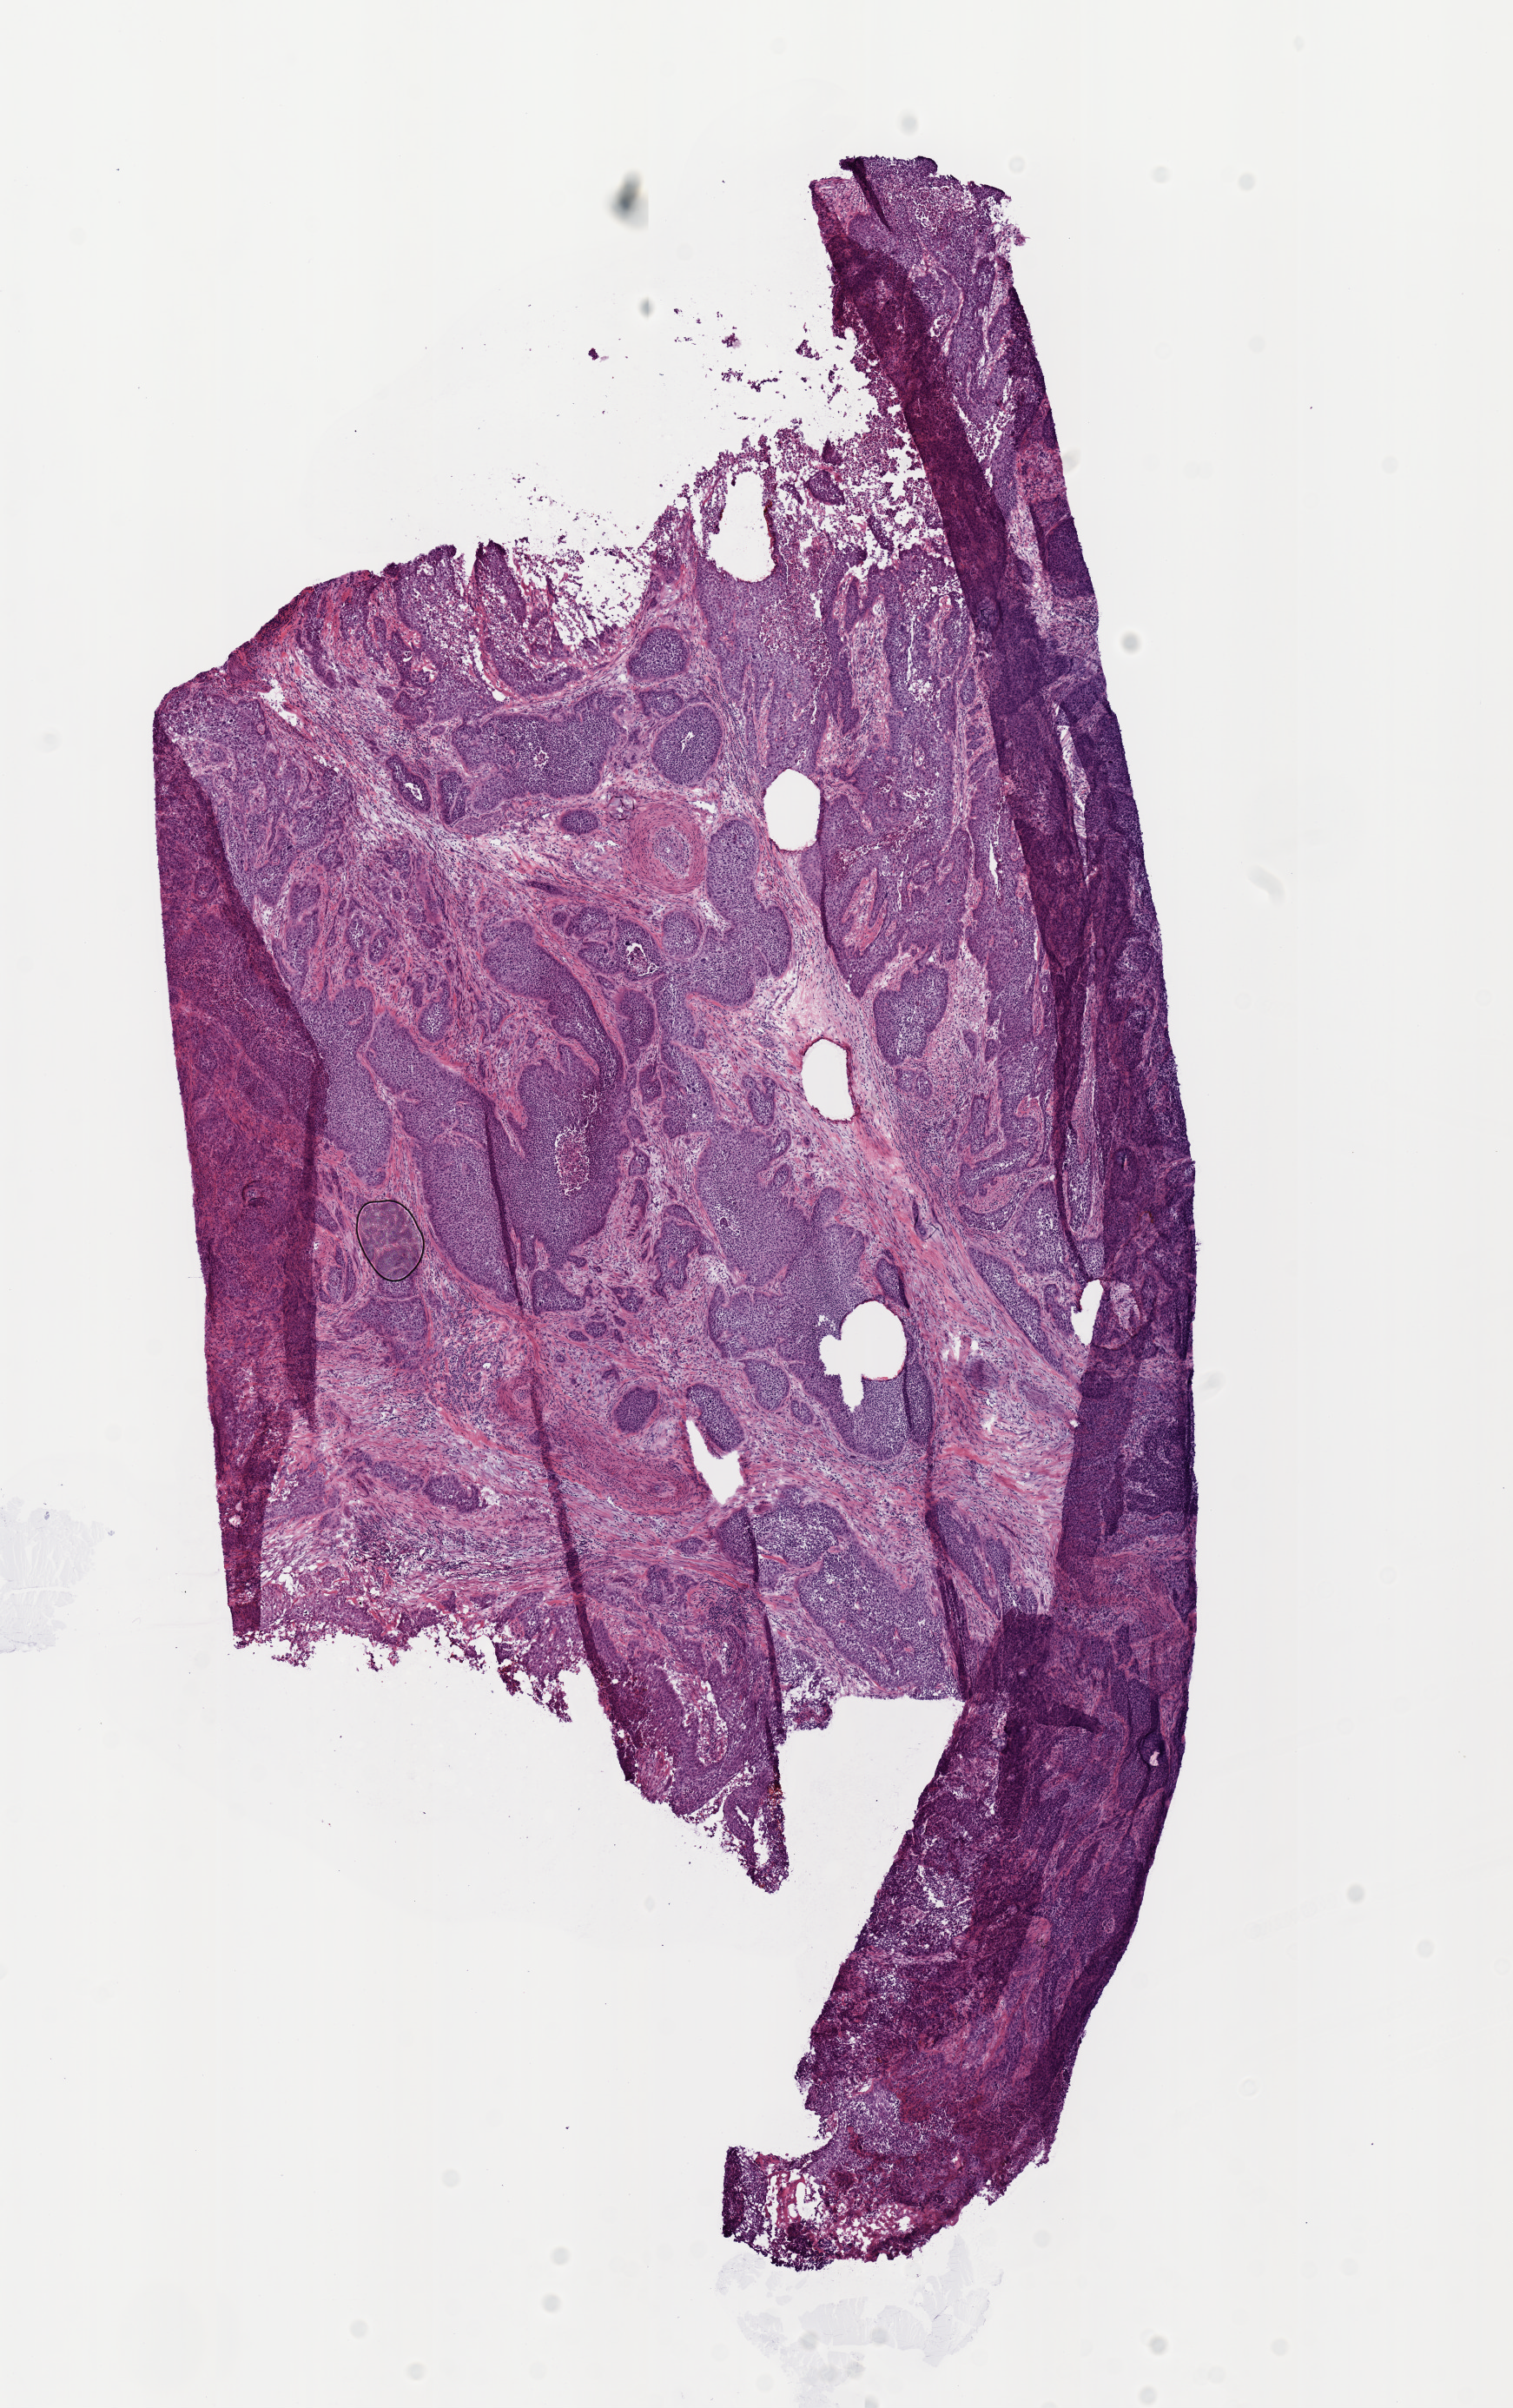
Digitized H&E tissue section (whole slide), a low-resolution overview of the entire scanned area, about 6.9 x 11.0 mm, frozen section from the top of the tissue portion, cervix, primary tumour sample. Female, age 47 years at initial diagnosis. Histologic grade: G2 (moderately differentiated). Pathologist review of this section (percent, as recorded): tumour nuclei 75%, normal cells 0%, stromal cells 15%, necrosis 5%. Inflammatory infiltration, as recorded: lymphocyte infiltration 0%, monocyte infiltration 0%, neutrophil infiltration 0%.
* pathologic diagnosis: Squamous cell carcinoma, large cell, nonkeratinizing, NOS (cervix uteri)
* FIGO stage: IB2